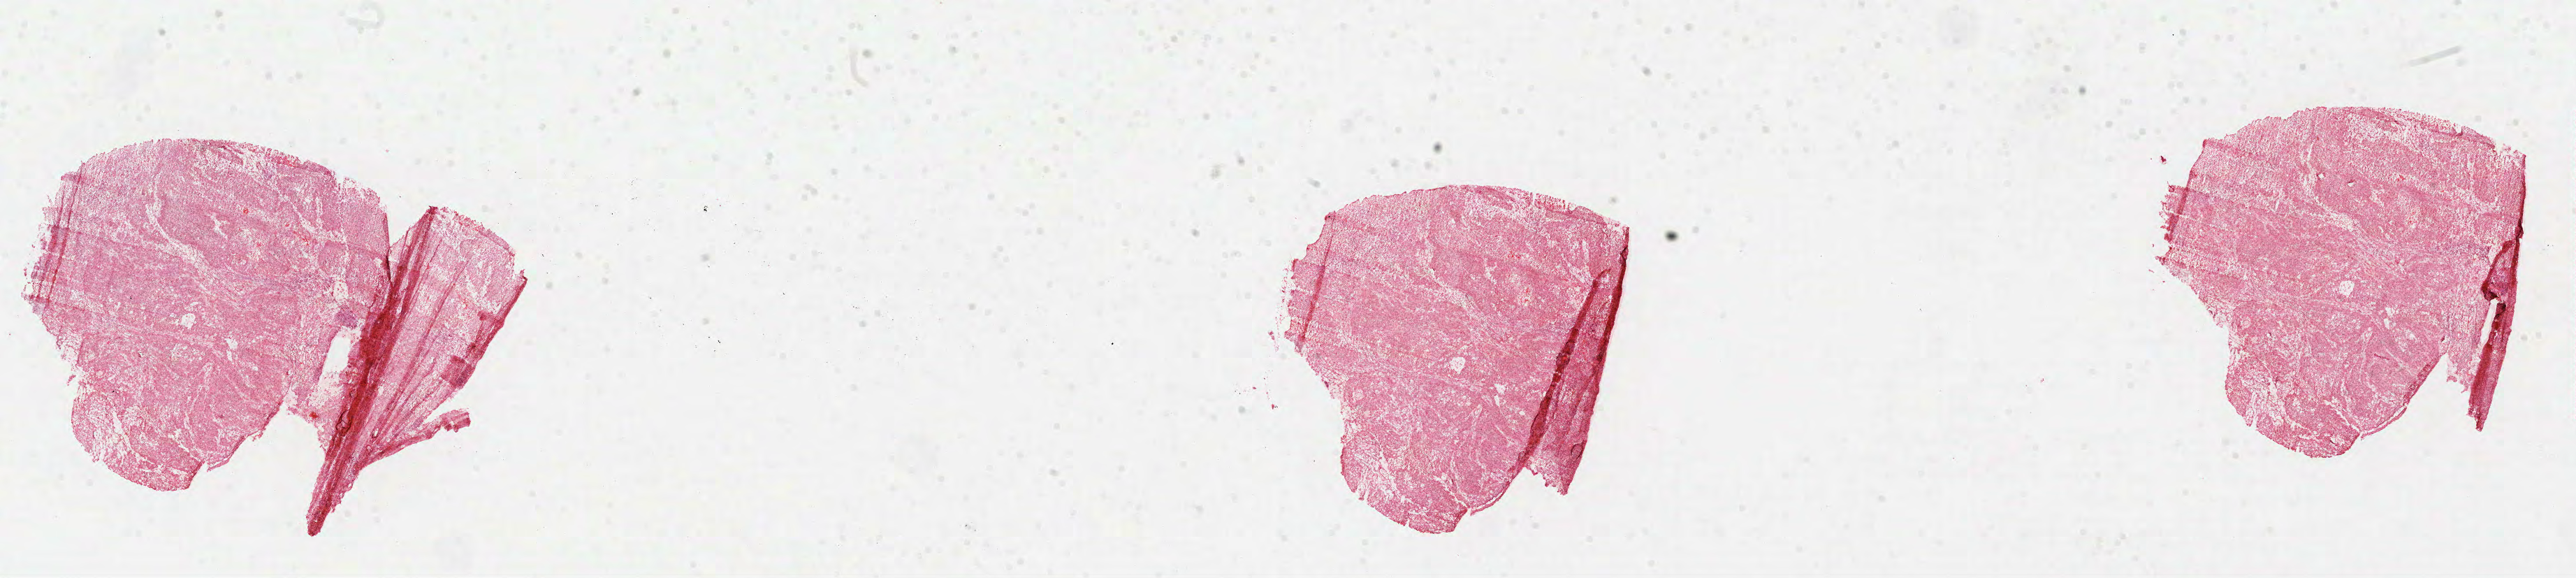
Digitized H&E tissue section (whole slide) — whole scanned area (about 29.7 x 6.7 mm, acquisition: 40x scan) shown as a low-resolution overview; formalin-fixed paraffin-embedded (FFPE) diagnostic section; head and neck, primary tumour sample. Patient: male, age at initial diagnosis 50 years. Histologic grade: G2 (moderately differentiated).
AJCC pathologic stage: II (7th edition). Pathologic diagnosis: Squamous cell carcinoma, NOS (tongue, NOS).